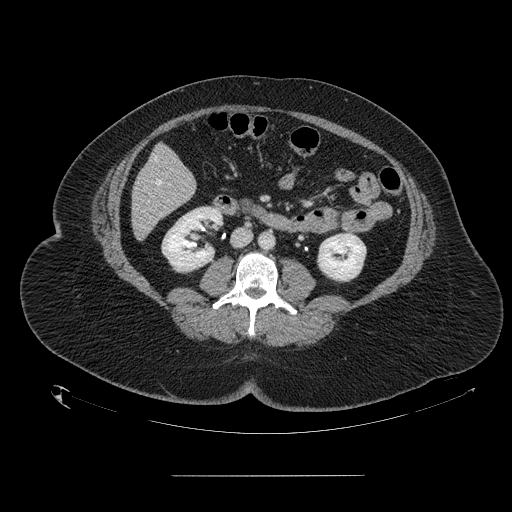
Contrast-enhanced abdominal CT, one axial slice; slice 42 of 164 in the series (ordered by position); 120 kVp; intravenous contrast given; soft-tissue window (W 400 / L 40 HU); 2.5 mm slice thickness; 512 × 512 image matrix. Female patient, age 52 years. Case-level facts recorded for this patient, not image findings: diagnosis: colorectal cancer liver metastases, imaged before liver resection; multiple liver metastases: yes; largest metastasis: 3.5 cm.
Outlined on this slice (outlined manually by an expert reader):
- hepatic veins: box from (x=154, y=159) to (x=161, y=185) px
- liver: (x=132, y=146)–(x=196, y=239)